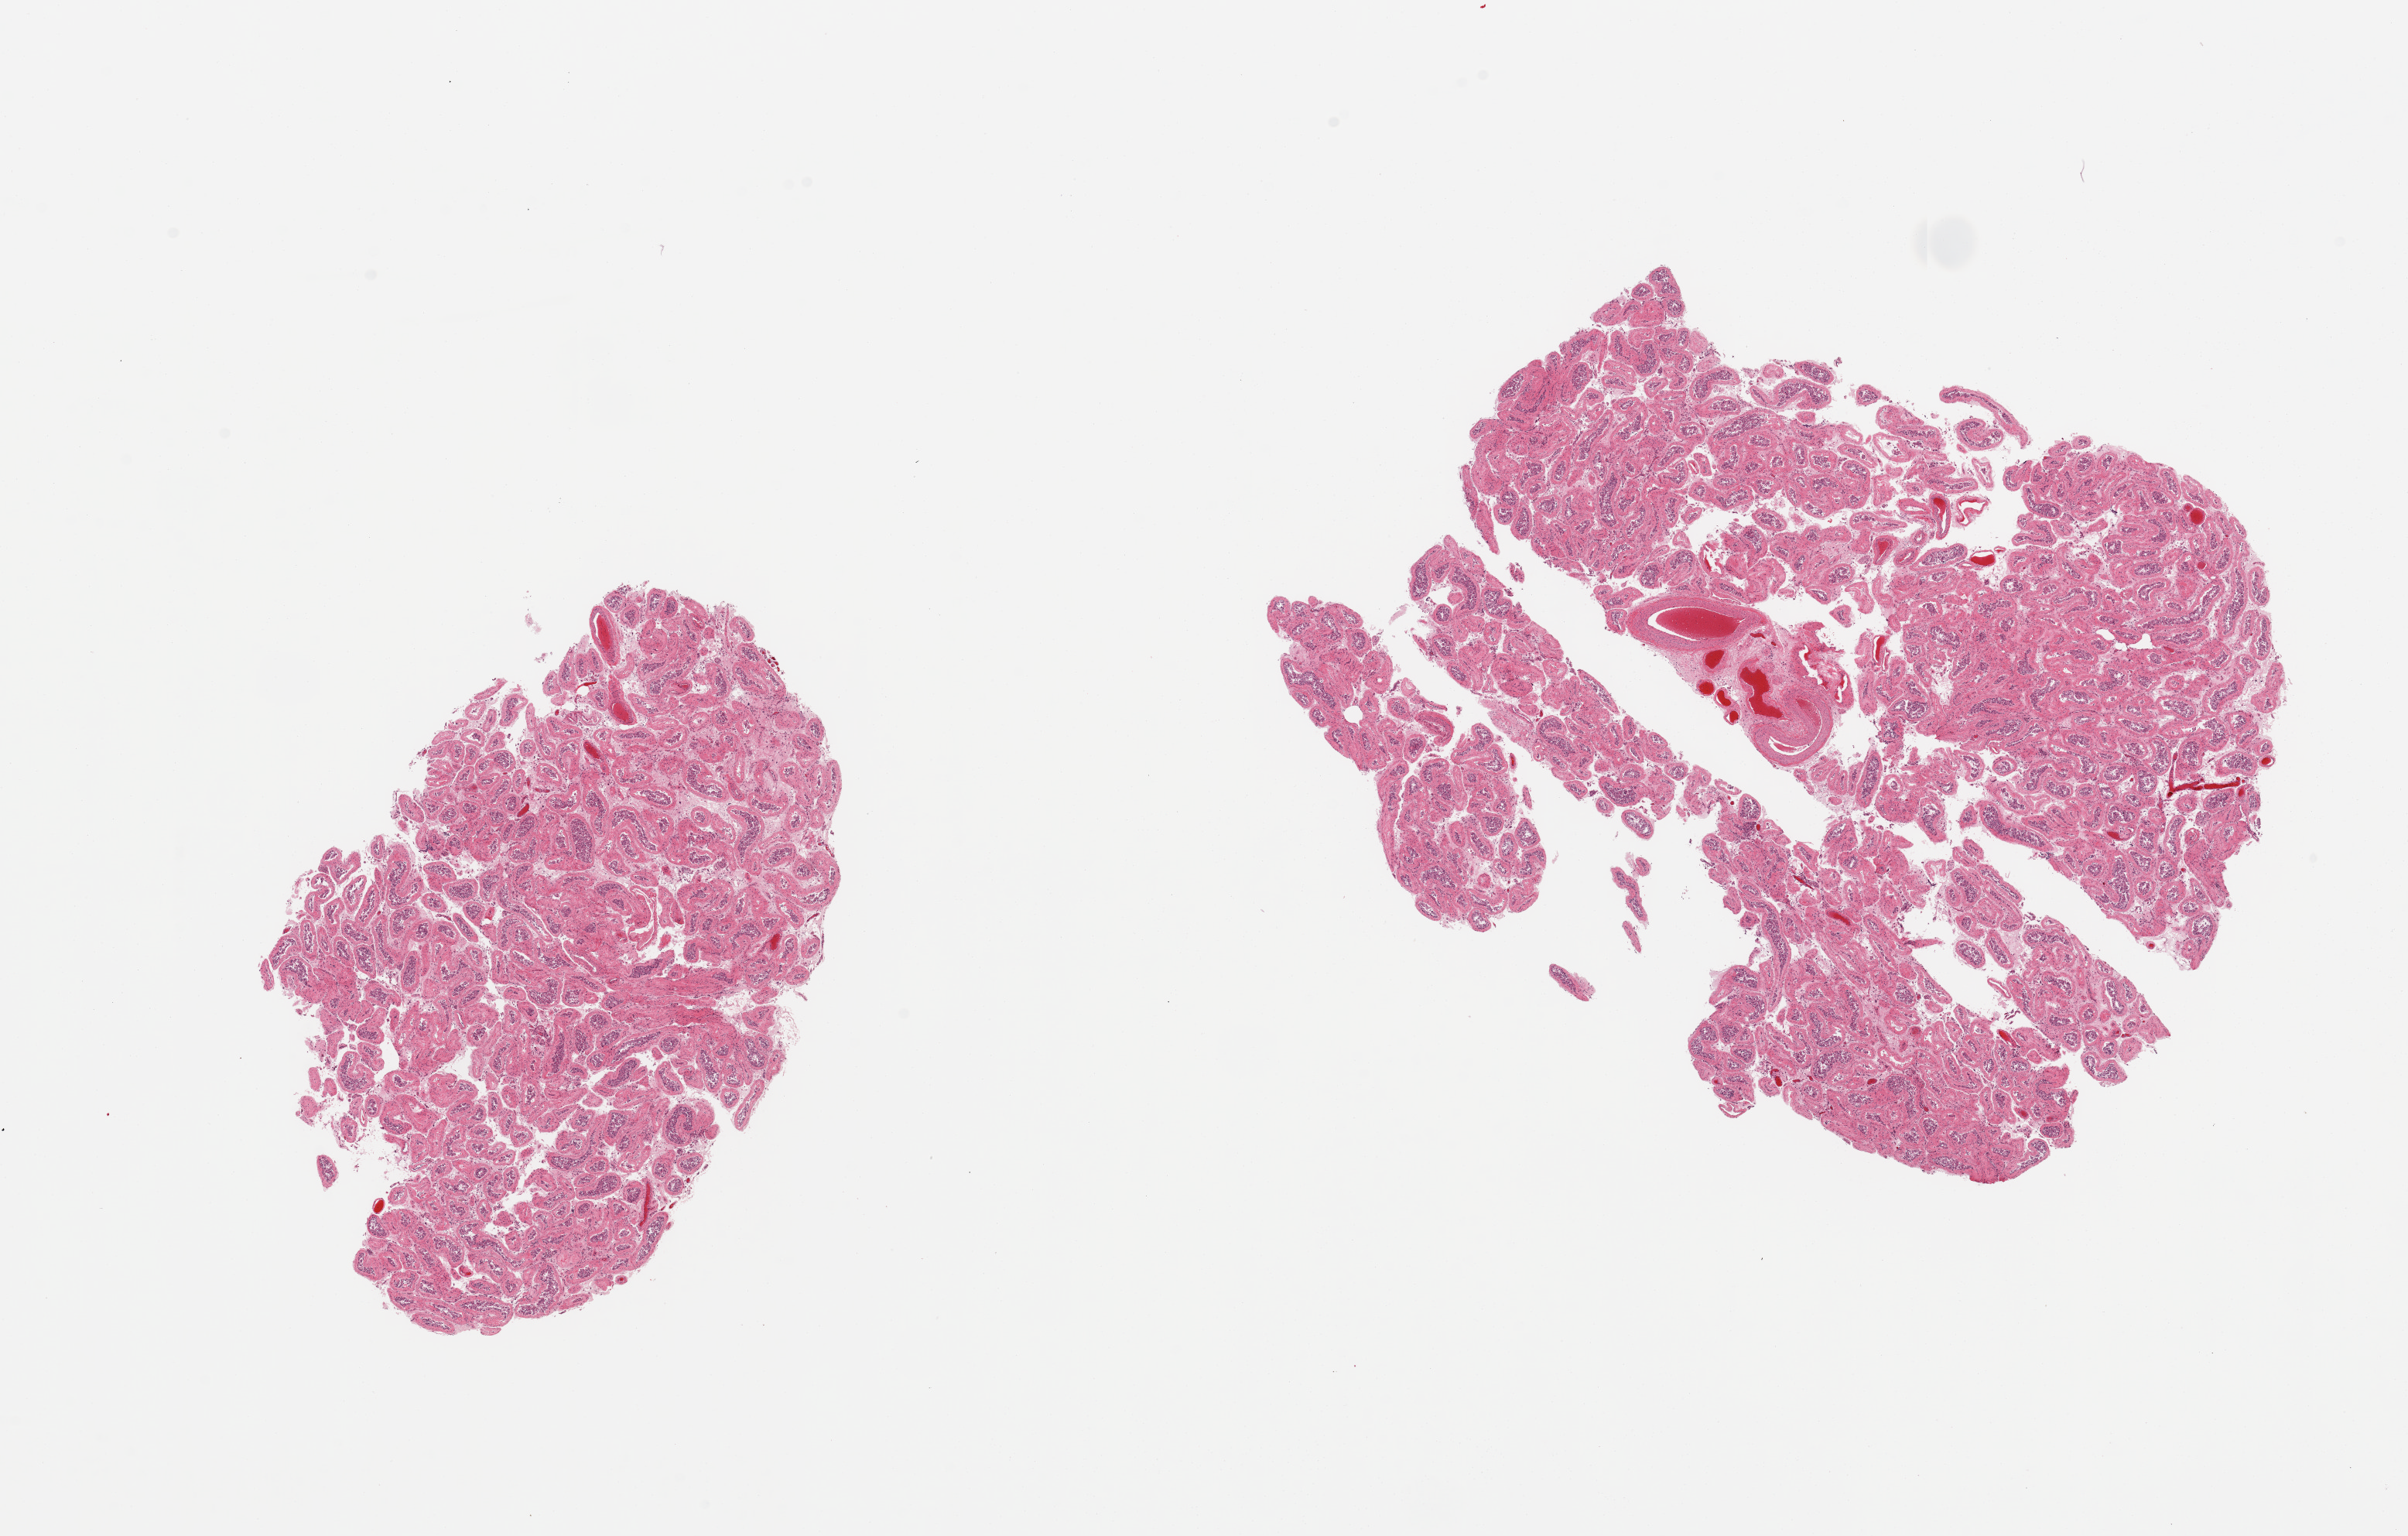
Hematoxylin and eosin (H&E) whole-slide image — a low-resolution overview of the entire scanned area, about 24.6 x 15.7 mm (slide scanned at 20x). PAXgene-fixed, paraffin-embedded tissue. Target tissue: testis. Tissue donor sample. Donor sex: male.
Review note (as recorded): 2 pieces; thickening of tubular basement membrane; arrest of spermatogenesis, Sertoli cells remain.